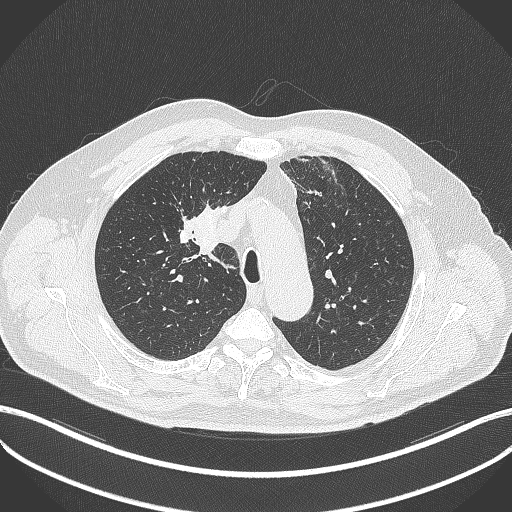
Chest CT, one axial slice; 120 kVp; lung window (W 1500 / L -600 HU); 1 mm slice thickness; 512 × 512 image matrix, field of view 400 × 400 mm. Male patient, age 60 years. Case-level facts recorded for this patient, not image findings: clinical TNM (as recorded): T1b N1 M0.
Structures marked on this image (rectangle marked by the reading radiologist):
- lung tumour (recorded histology: squamous cell carcinoma): bounding box [x1, y1, x2, y2] px = [197, 200, 225, 255]